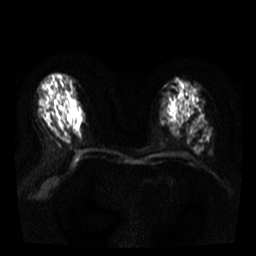
Breast MRI, one axial slice; position 16 of 38 along the scan axis; diffusion-weighted series; image 2 of 4 stored at this slice position (different b-values; order by instance number); 3 T; 5 mm slice thickness; 256 × 256 image matrix, field of view 320 × 320 mm. Female patient.
Structures marked on this image (outlined manually by an expert reader):
- tumour on diffusion-weighted imaging: box from (x=196, y=148) to (x=203, y=153) px